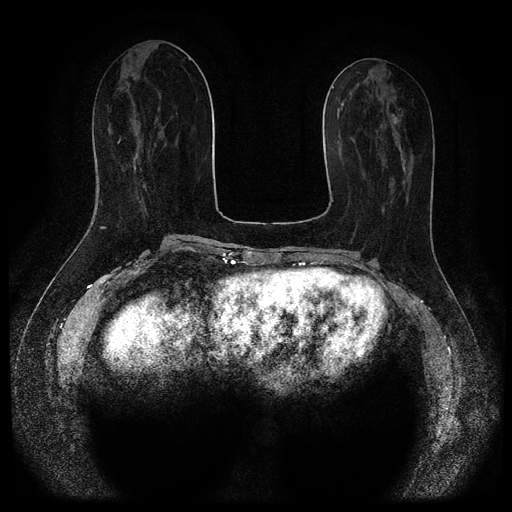
Breast MRI (dynamic contrast-enhanced, multi-phase), one axial slice. Slice 41 of 116 in the series (ordered by position). Dynamic contrast-enhanced series, time point 2 of 5 at this slice position (early post-contrast). 1.5 T. TE 2.7 ms, TR 5.4 ms. 2 mm slice thickness. 512 × 512 image matrix, field of view 340 × 340 mm. Female patient, age 47 years.
Annotated regions visible in this slice (semi-automatically segmented with operator editing):
- breast lesion (labelled benign in the annotation): bounding box [x1, y1, x2, y2] px = [390, 113, 399, 125]